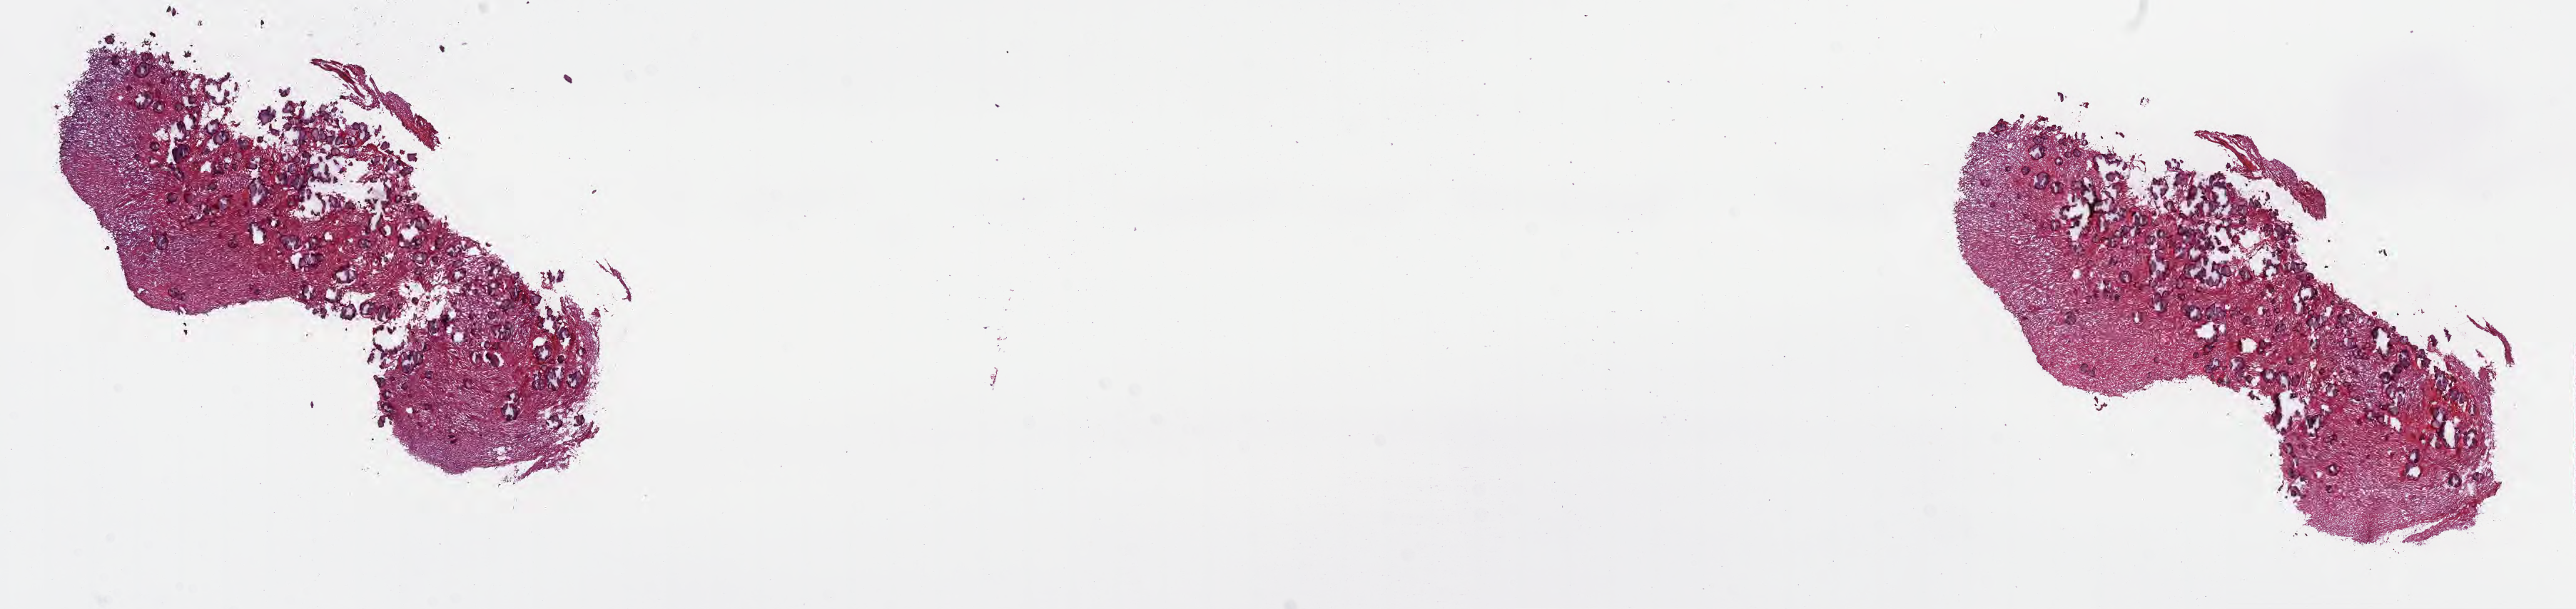
Whole-slide image, hematoxylin and eosin (H&E) stain of tumor tissue from the brain, a low-resolution overview of the entire scanned area, about 29.2 x 6.9 mm; frozen section (OCT-embedded). Patient male; age 164 months (13 years 8 months).
Diagnosis (ICD-O-3 morphology term): Neoplasm, uncertain whether benign or malignant.